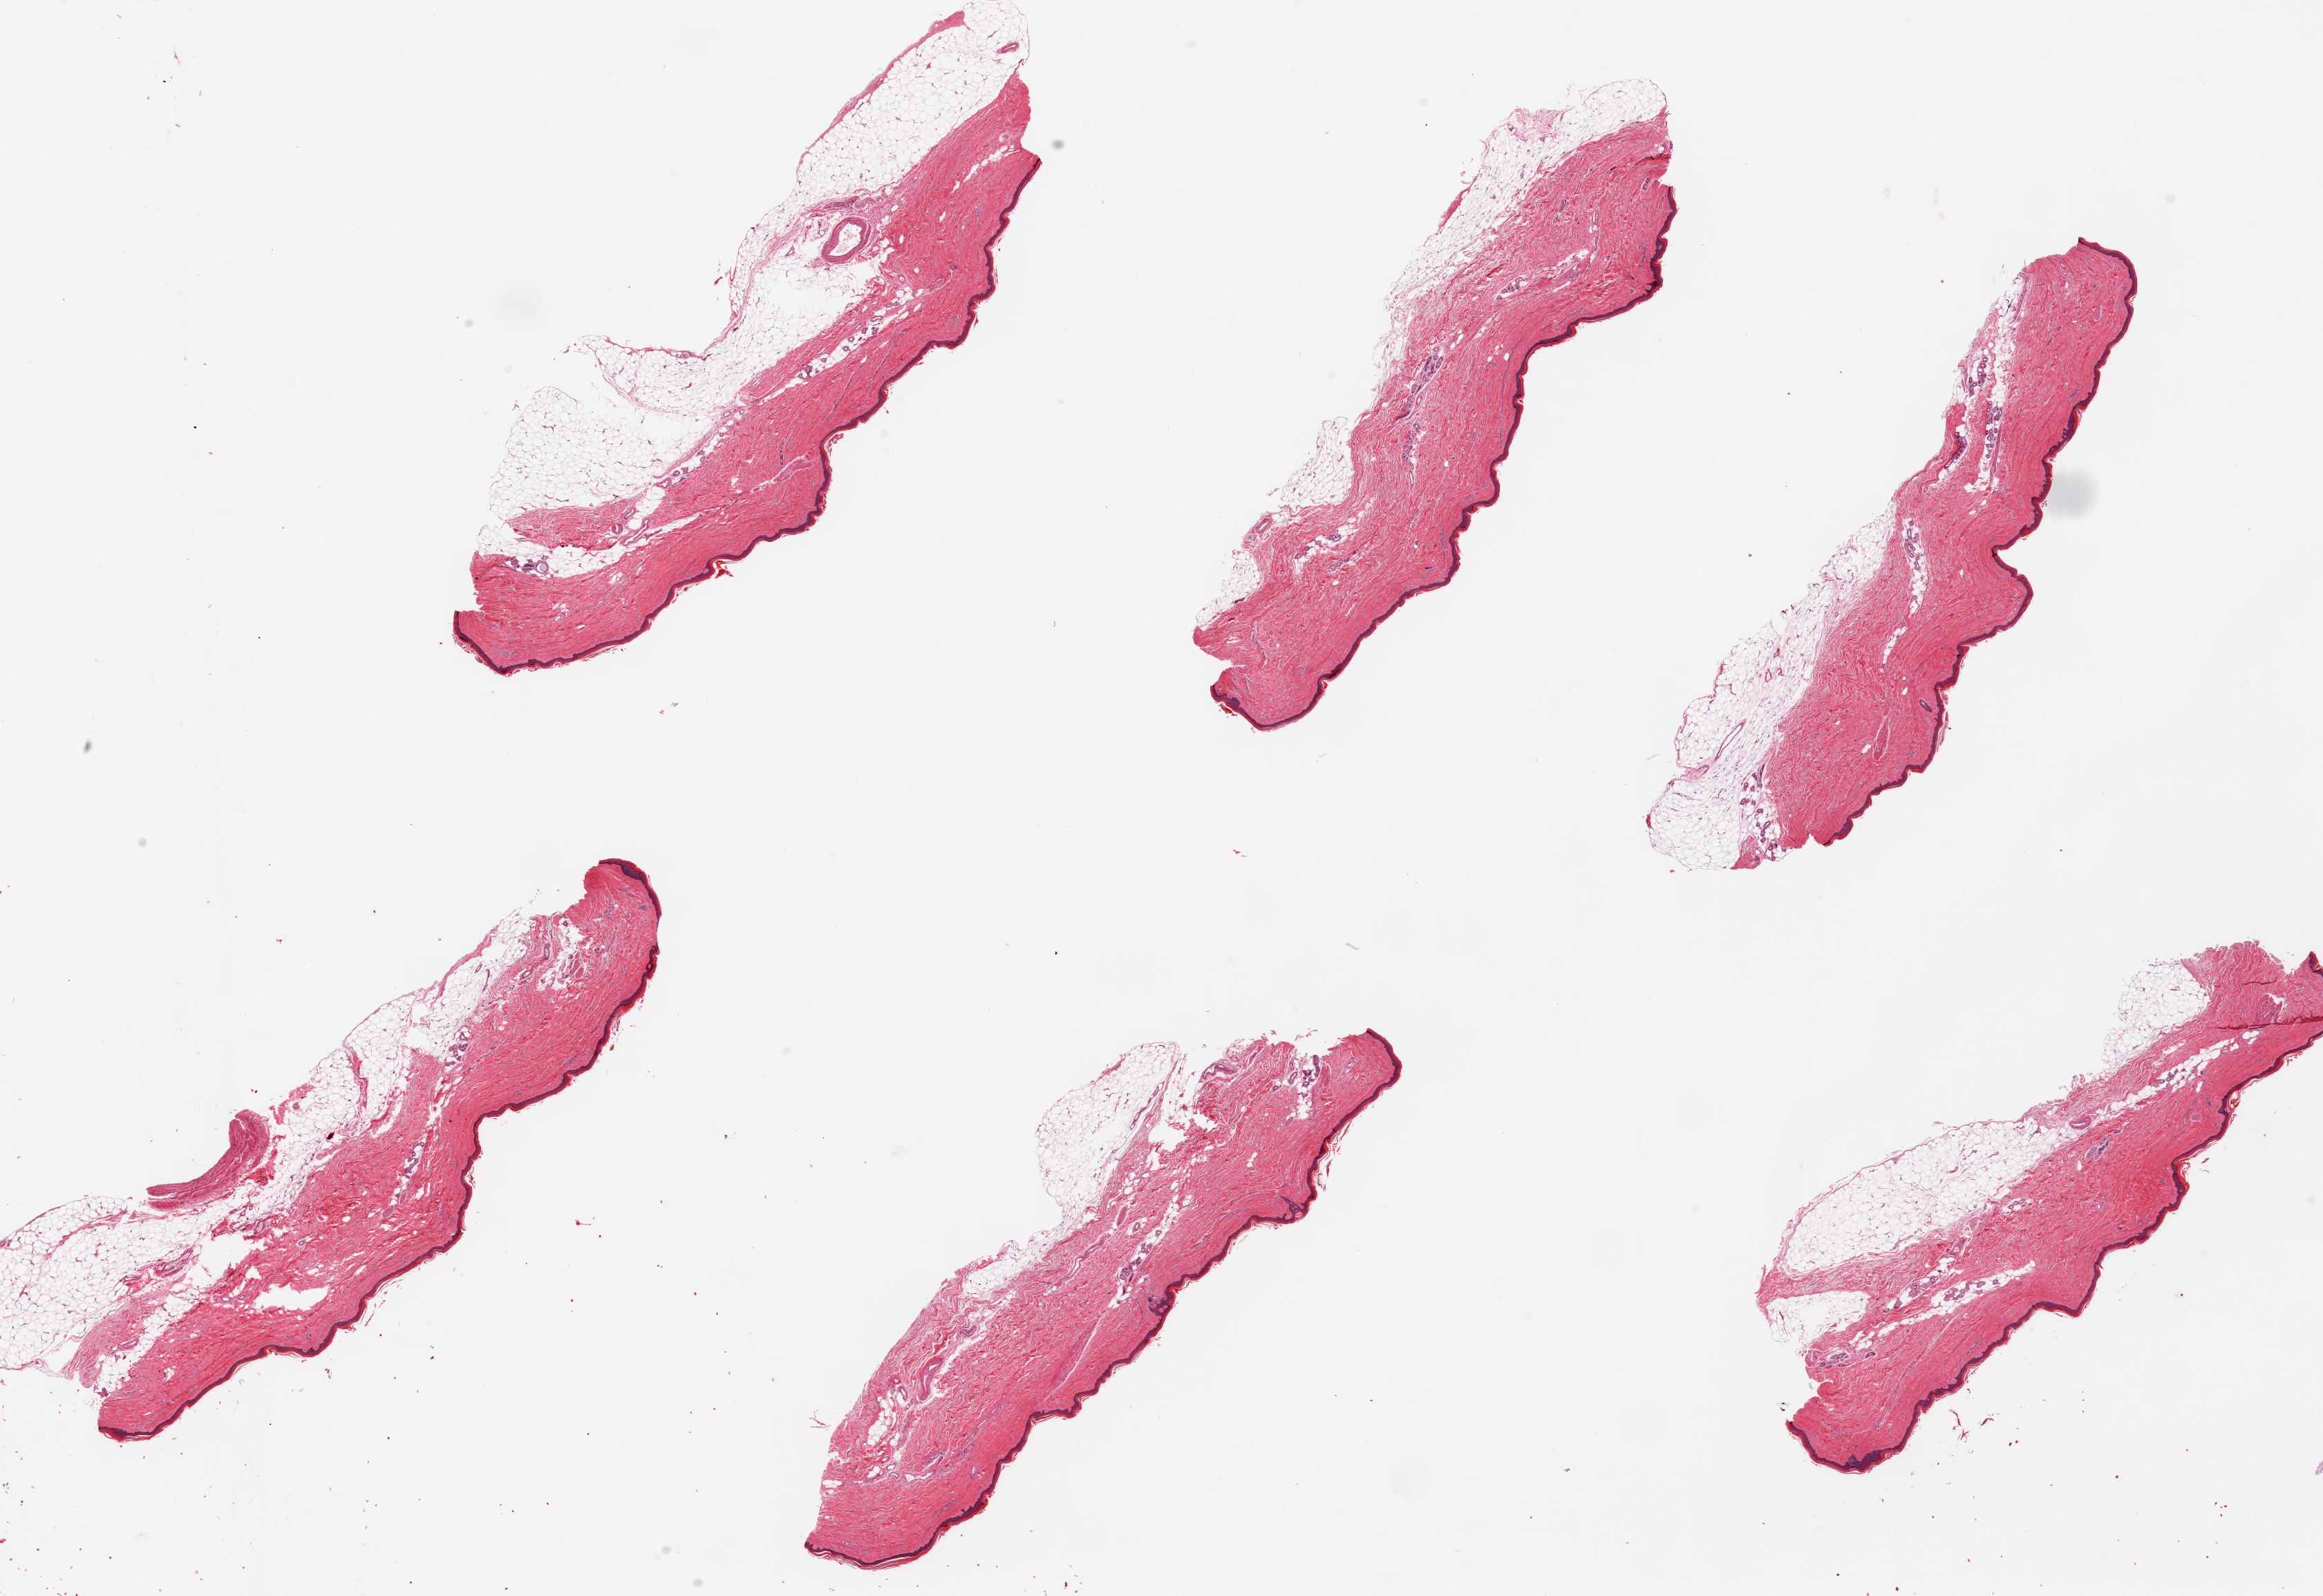
Hematoxylin and eosin (H&E) whole-slide image — low-resolution overview of the scanned area, about 26.6 x 18.3 mm, PAXgene-fixed paraffin-embedded (PFPE) section, target tissue: skin of lower leg, donor tissue sample.
Review note (as recorded): 6 pieces, up to 8x3.5mm; All have considerable subcutaneous adipose up to 3.5x 1 mm.